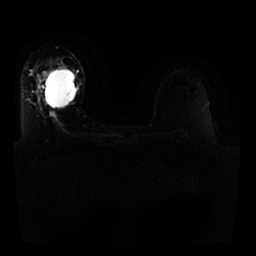
Breast MRI, one axial slice. Position 14 of 25 along the scan axis. Diffusion-weighted series; image 2 of 4 stored at this slice position (different b-values; order by instance number). 1.5 T. 256 × 256 image matrix, field of view 330 × 330 mm. Female patient.
Annotated regions visible in this slice (manually delineated by an expert):
- tumour on diffusion-weighted imaging: bounding box <46,69,57,78> (left, top, right, bottom; pixels)